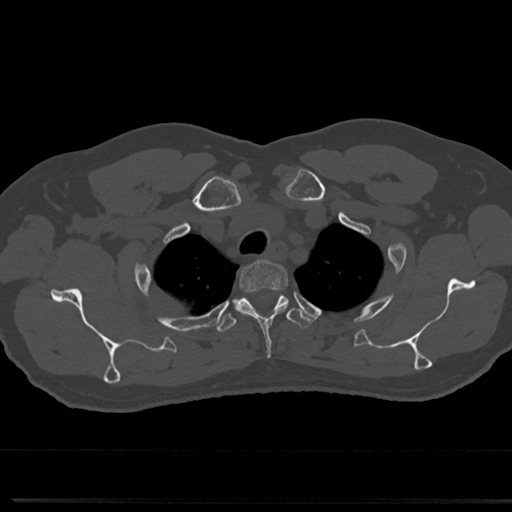
CT including the spine, one axial slice. Position 614 of 817 along the scan axis. Bone window (W 1800 / L 400 HU). 512 × 512 image matrix. Patient: male, 61 years. From the clinical record (not read from this slice): primary cancer: prostate.
Structures marked on this image (semi-automatically segmented with operator editing):
- T2 vertebra: box from (x=239, y=261) to (x=289, y=289) px
- T3 vertebra: (x=214, y=291)–(x=312, y=334)